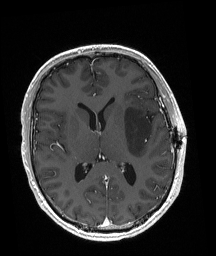
Brain MRI from a brain-tumour surgery series, one axial slice; position 94 of 192 along the scan axis; T1-weighted post-contrast; 1 mm slice thickness; 216 × 256 image matrix, field of view 211 × 250 mm. Case-level facts recorded for this patient, not image findings: histopathology: Astrocytoma; WHO grade: 3.
Annotated regions visible in this slice (manually delineated by an expert):
- tumour: bounding box [x1, y1, x2, y2] px = [124, 108, 152, 157]